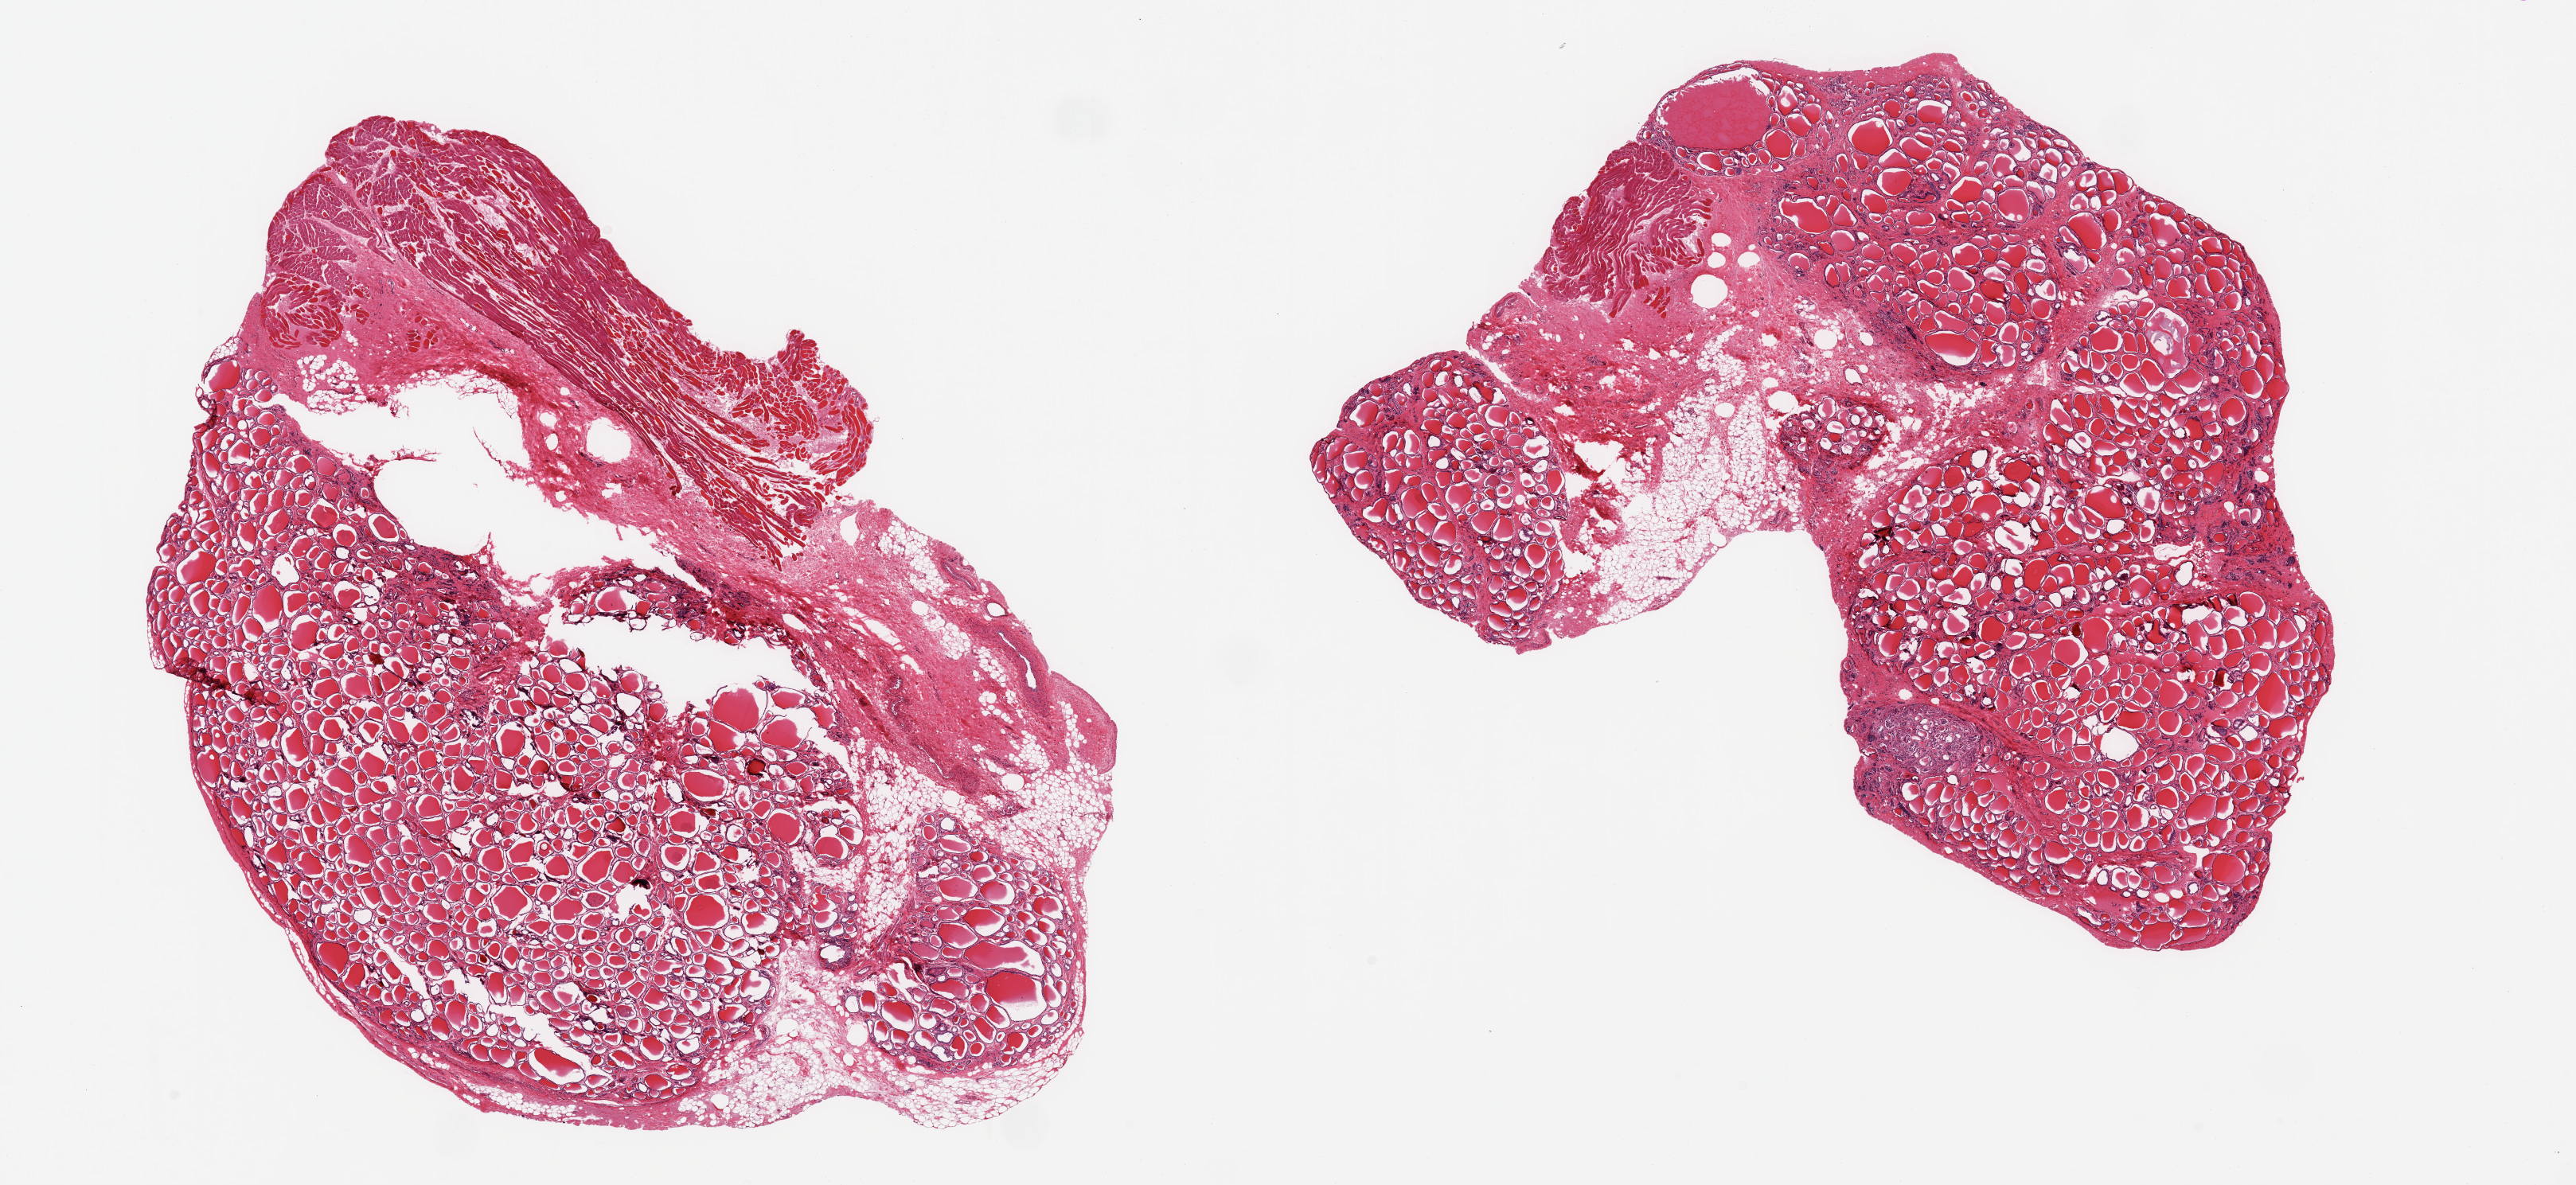
Whole-slide image, H&E stain — a low-resolution overview of the entire scanned area, about 25.6 x 11.8 mm (slide scanned at 20x); PAXgene-fixed paraffin-embedded (PFPE) section; target tissue: thyroid; donor tissue sample. Donor sex: female.
Reviewer comment on this tissue sample: 2 pieces; mild to moderate autolysis; 40% and 30% attached skeletal muscle and fibroadipose tissue.